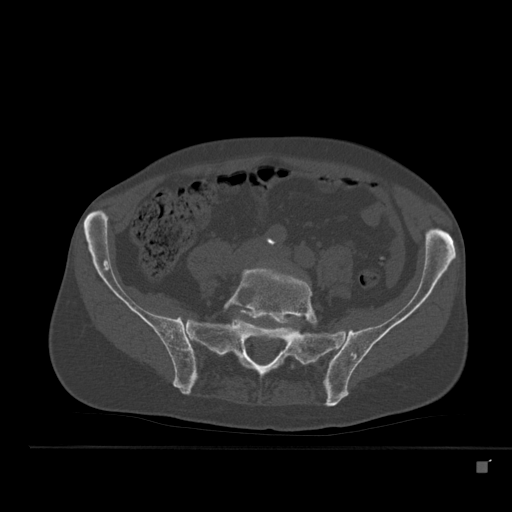
CT including the spine, one axial slice; slice 118 of 517 in the series (ordered by position); reconstruction kernel Br40s; bone window (W 1800 / L 400 HU); 1.5 mm slice thickness; 512 × 512 image matrix, field of view 408 × 408 mm. Male patient, age 70 years. Case-level facts recorded for this patient, not image findings: primary cancer: renal; vertebrae with lytic lesions (as recorded): T4, T6, T10, T12, L3, L4, L5.
Outlined on this slice (semi-automatic segmentation, software-assisted and operator-edited):
- L5 vertebra: bounding box (x1, y1, x2, y2) in pixels: (224, 267, 318, 369)